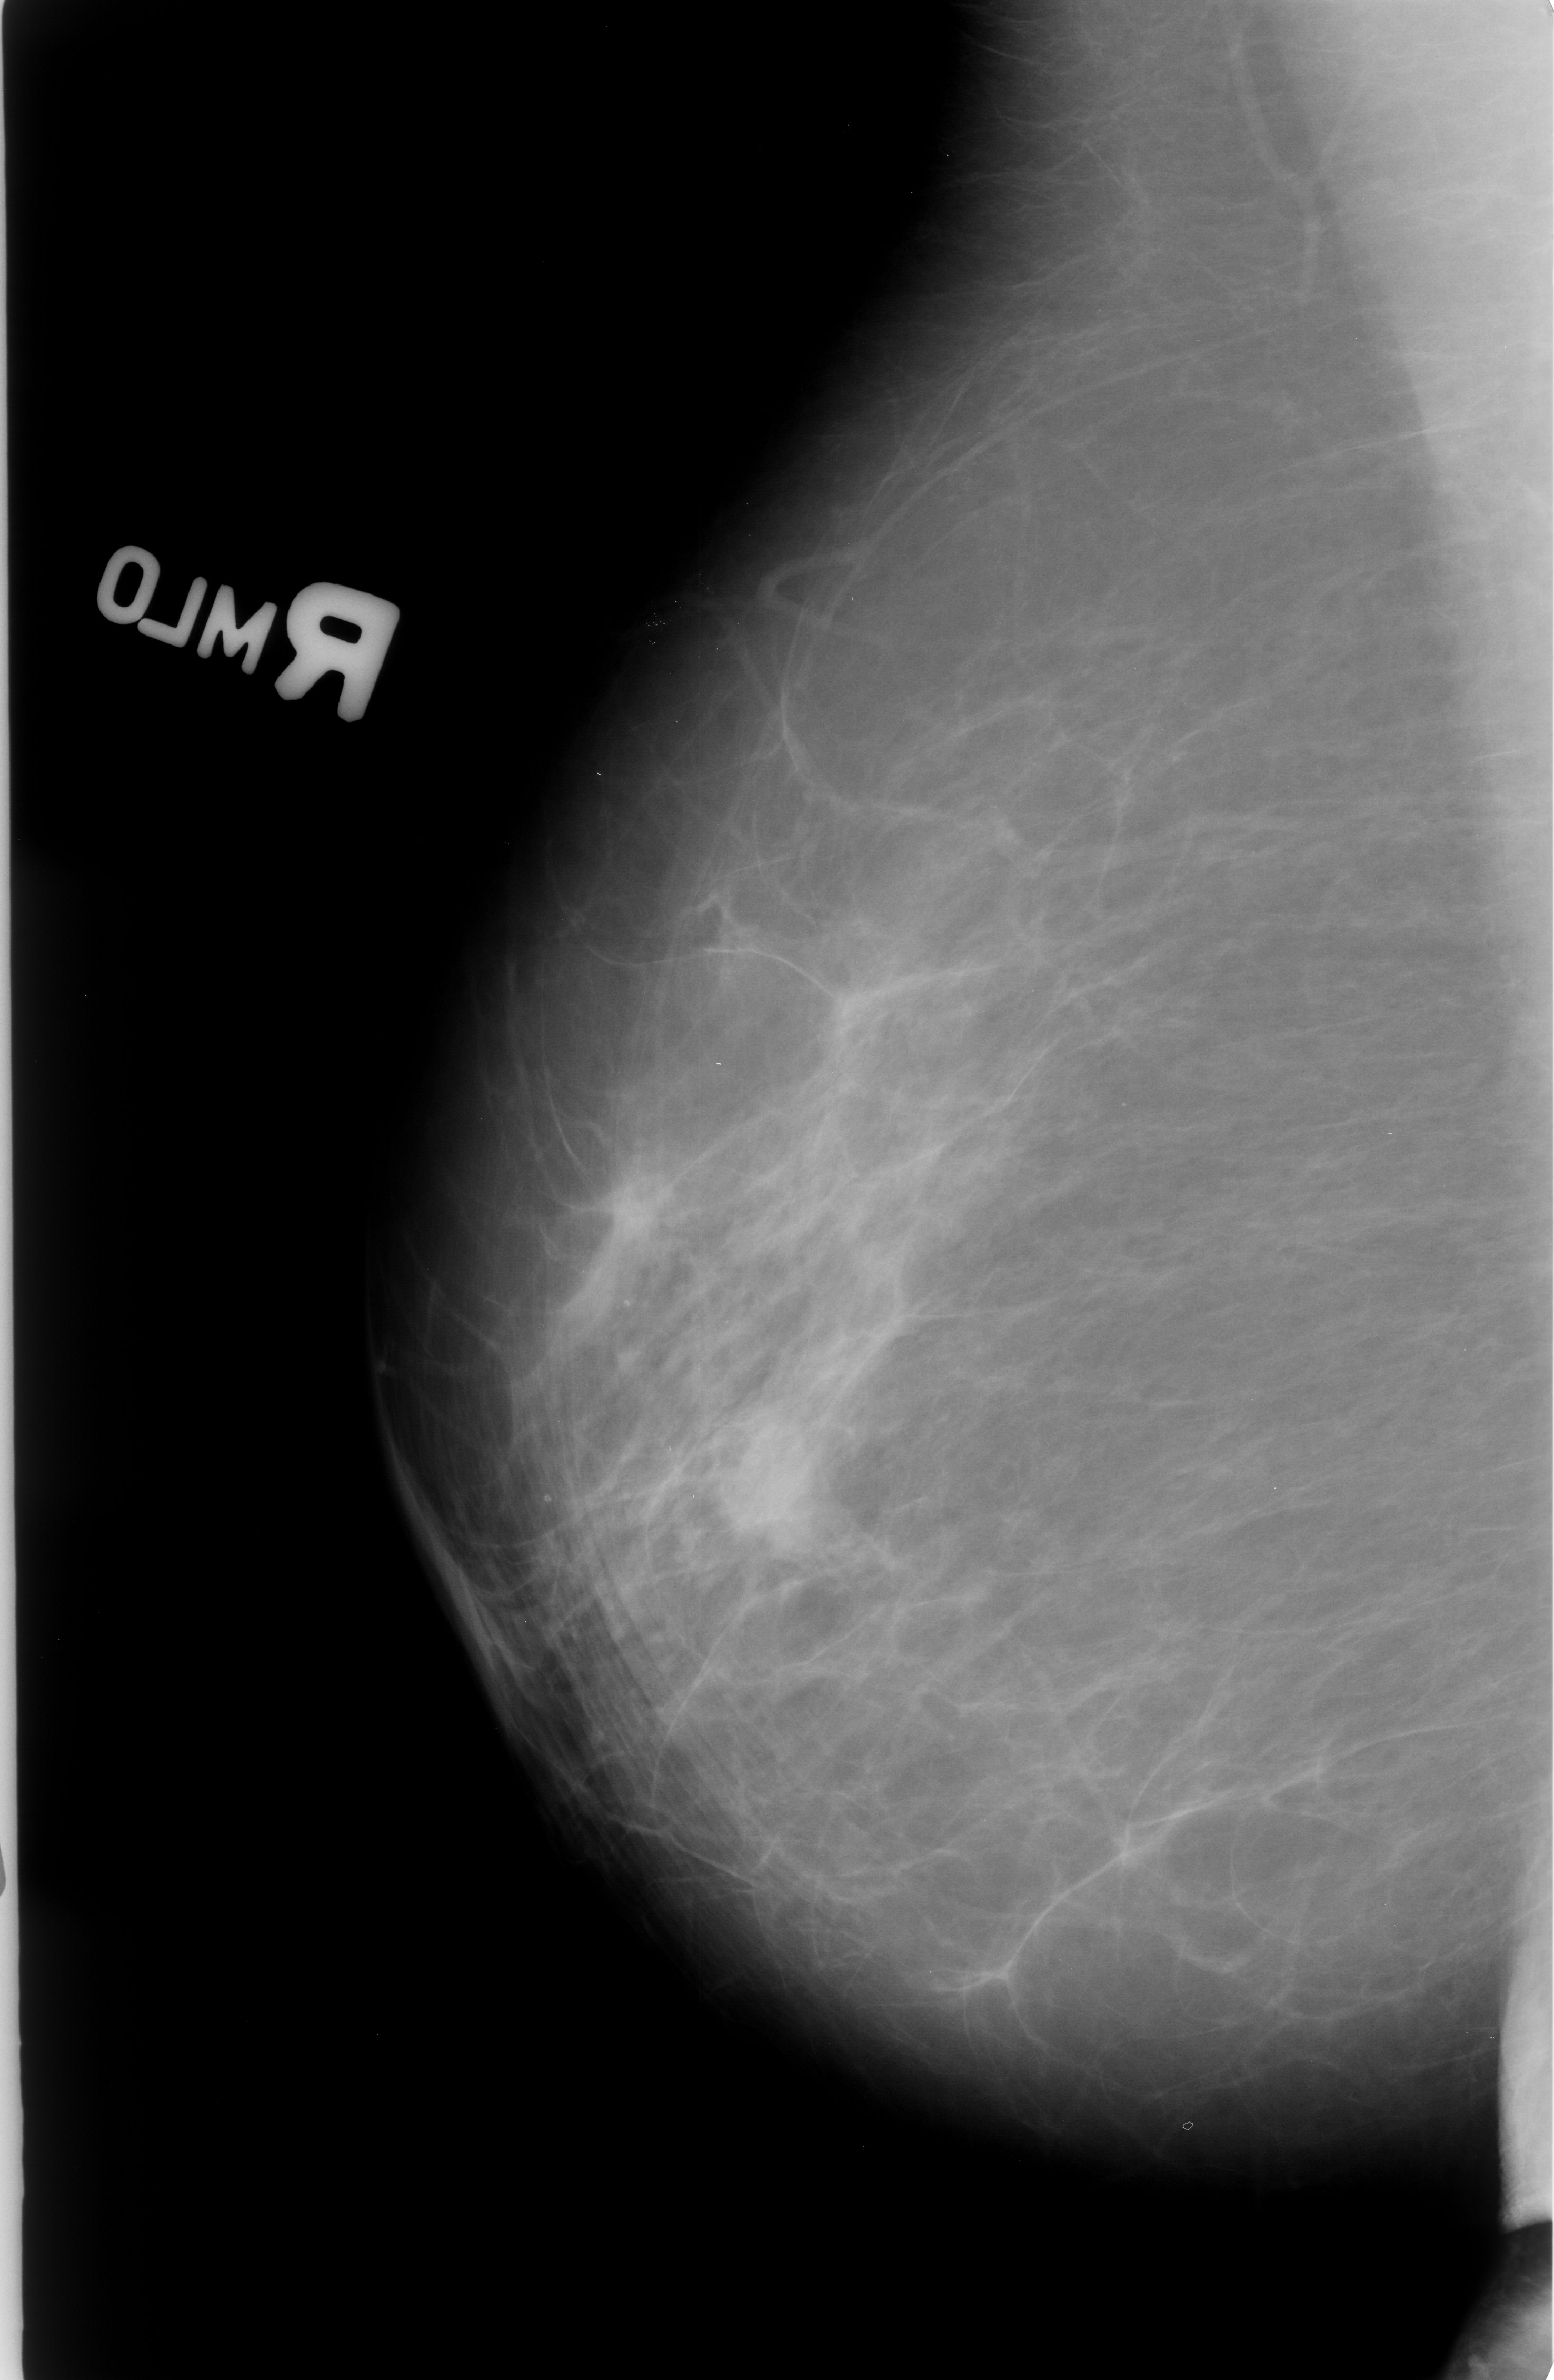
Mammogram (digitized film); right breast; MLO view; BI-RADS breast density category 2 (scale 1–4); 1554 × 2380 image matrix.
Expert-marked regions of interest on this film, with their recorded descriptors:
- mass, shape irregular, margins spiculated; BI-RADS assessment category 5; subtlety rating 4 on a 1 (subtle) to 5 (obvious) scale; pathology (as recorded): malignant: box from (x=718, y=1409) to (x=836, y=1563) px